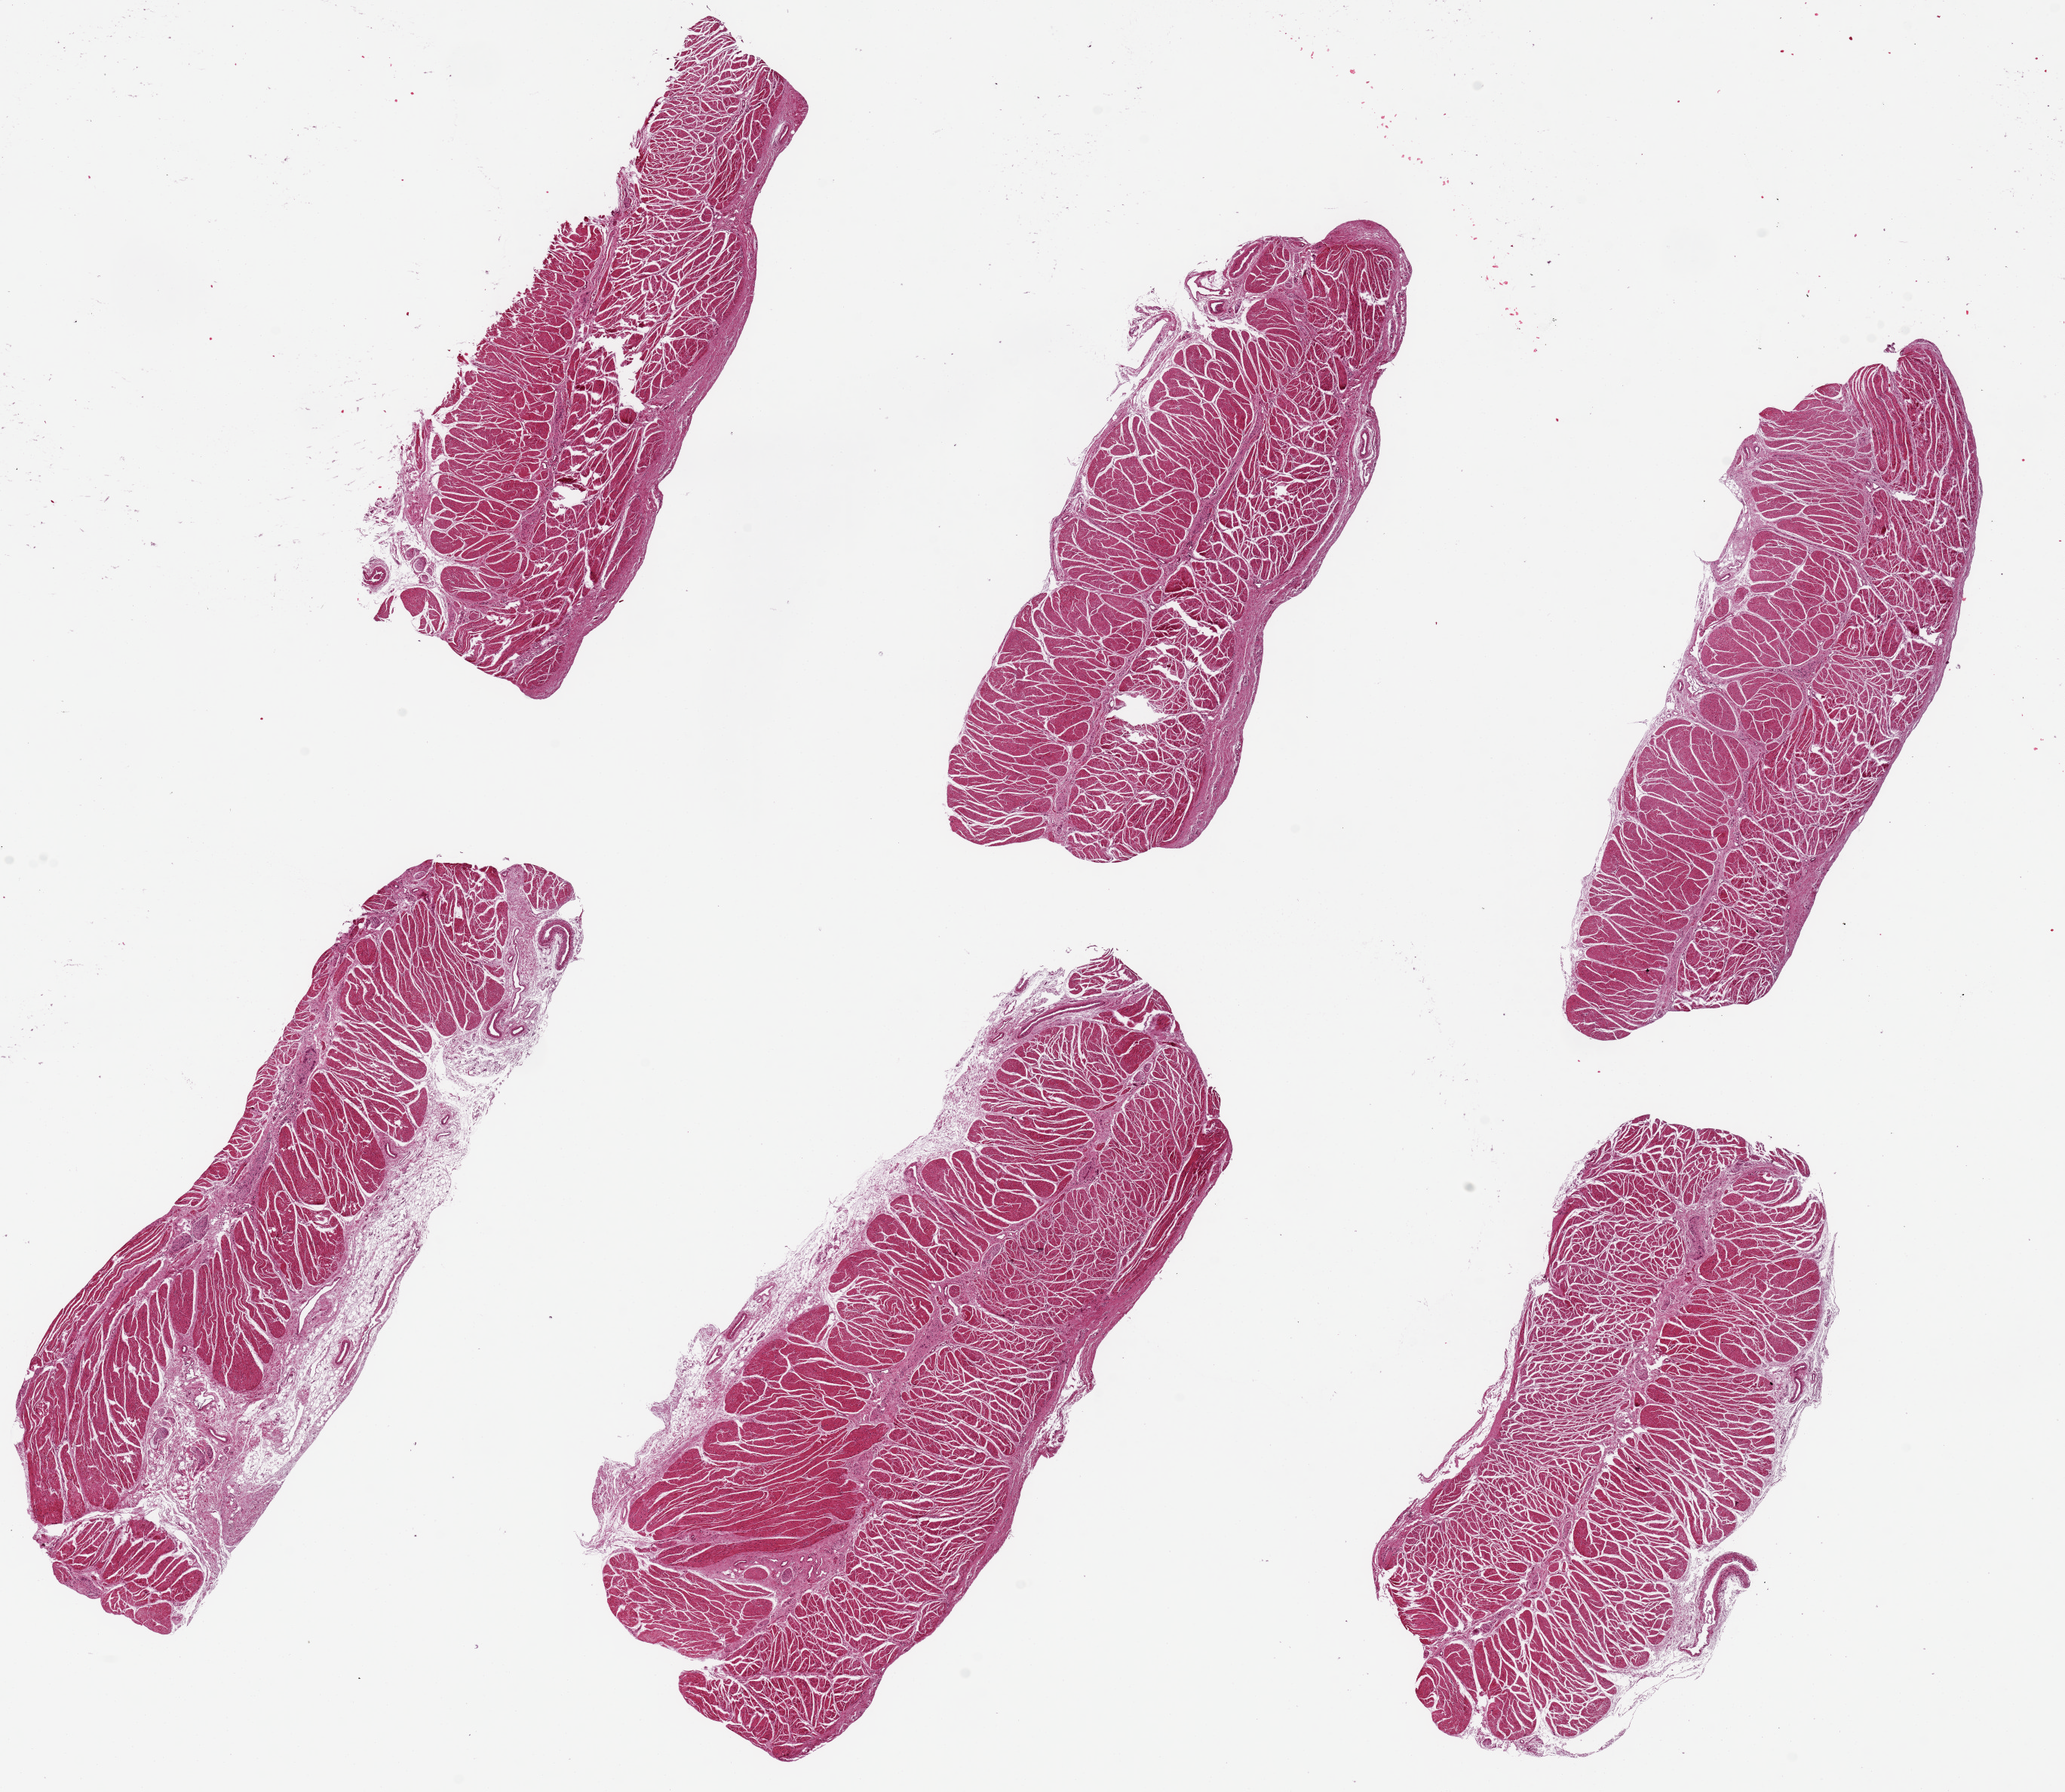
Whole-slide image, hematoxylin and eosin (H&E) stain, brightfield, shown as a low-resolution overview of the whole scanned area (about 21.7 x 18.8 mm), PAXgene-fixed, paraffin-embedded tissue, section of esophageal muscle (target tissue), donor tissue sample. Donor sex: female.
Reviewer comment on this tissue sample: 6 pieces, ~7x2.5mm.